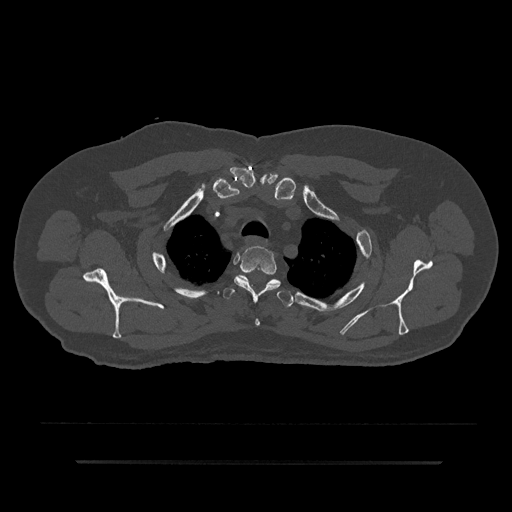
CT including the spine, one axial slice. Position 686 of 797 along the scan axis. Reconstruction kernel Br40s/3. Bone window (W 1800 / L 400 HU). 0.5 mm slice thickness. 512 × 512 image matrix. Patient: male, 59 years. Case-level facts recorded for this patient, not image findings: primary cancer: bile ducts; vertebrae with lytic lesions (as recorded): T10.
Annotated regions visible in this slice (semi-automatically segmented with operator editing):
- T2 vertebra: box from (x=234, y=246) to (x=281, y=326) px
- T3 vertebra: (x=223, y=285)–(x=293, y=307)